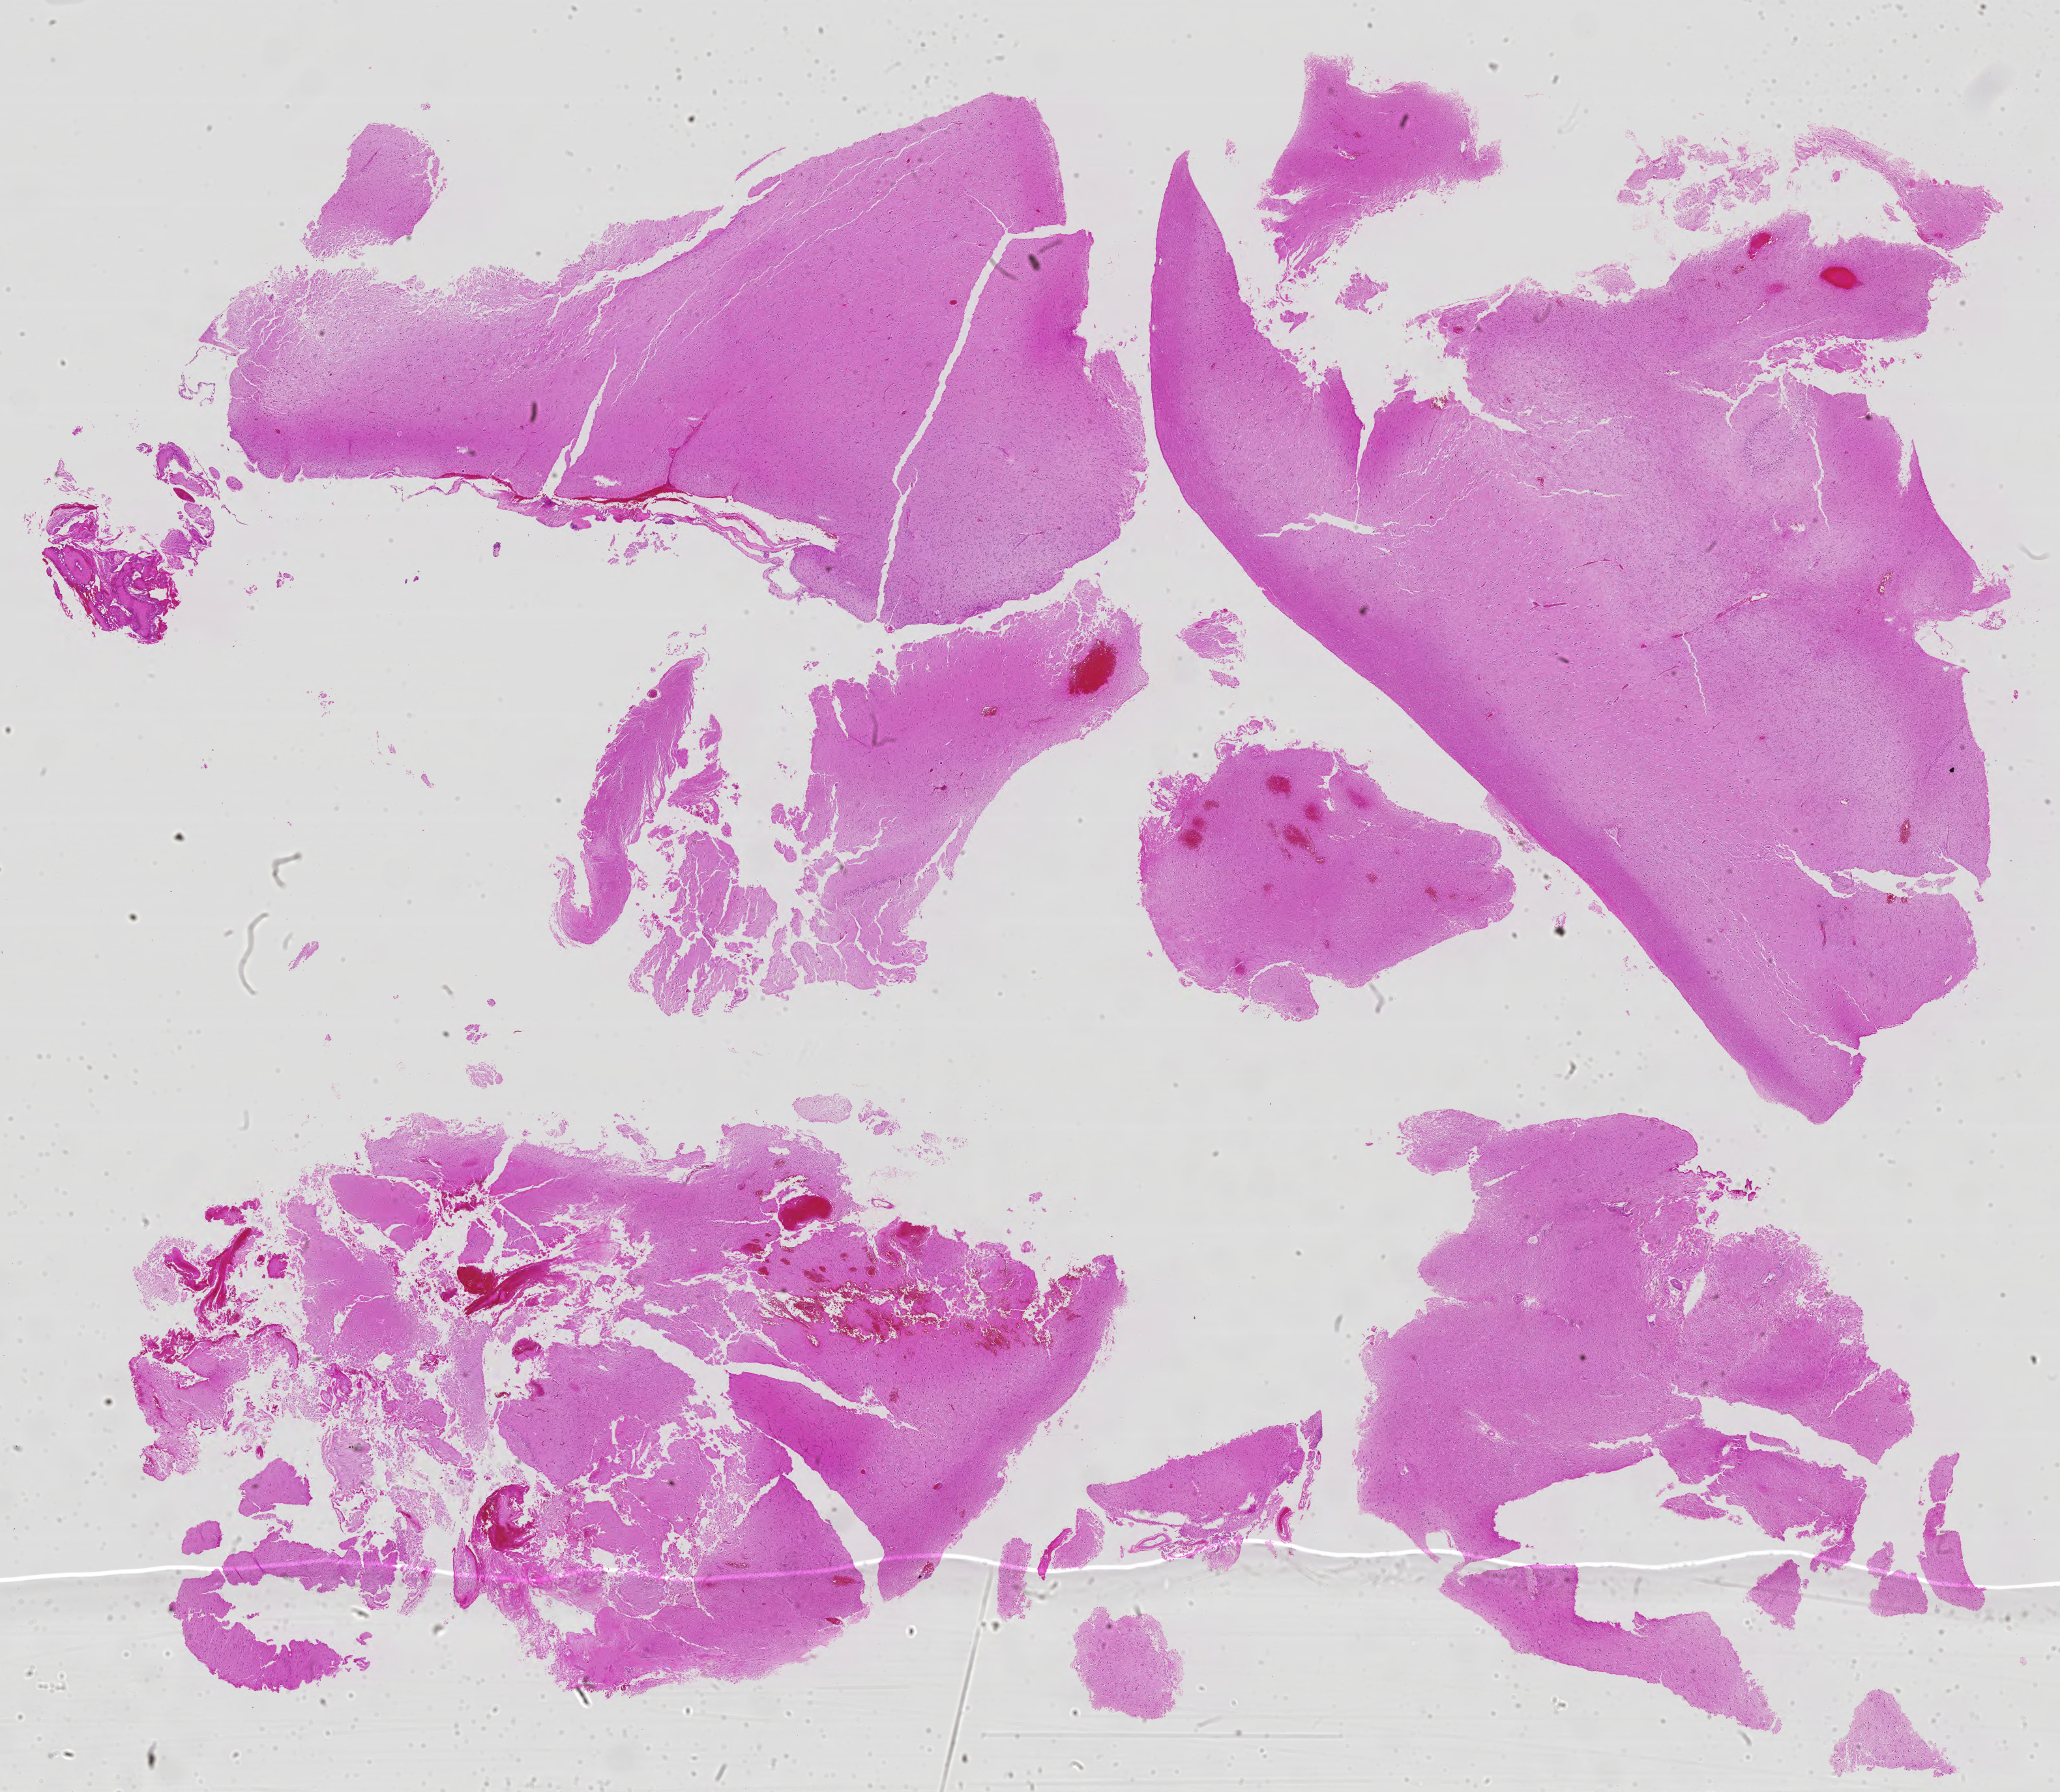
Whole-slide histology image, H&E-stained — low-resolution overview of the scanned area, about 25.3 x 22.0 mm; formalin-fixed paraffin-embedded (FFPE) diagnostic section; sample: primary tumour, brain. Male patient; age at initial diagnosis 63 years. Histologic grade: G3 (poorly differentiated).
Laterality: left. Diagnosis: Astrocytoma, anaplastic (cerebrum).